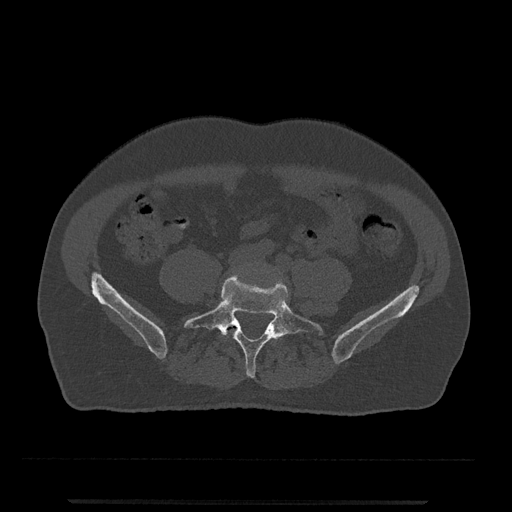
CT including the spine, one axial slice. Slice 82 of 797 in the series (ordered by position). Reconstruction kernel Br40s/3. Bone window (W 1800 / L 400 HU). 0.5 mm slice thickness. 512 × 512 image matrix, field of view 419 × 419 mm. Patient: male, 63 years. Case-level facts recorded for this patient, not image findings: primary cancer: prostate.
Annotated regions visible in this slice (semi-automatically segmented with operator editing):
- L4 vertebra: bounding box (x1, y1, x2, y2) in pixels: (226, 321, 237, 332)
- L5 vertebra: (183, 274, 323, 378)